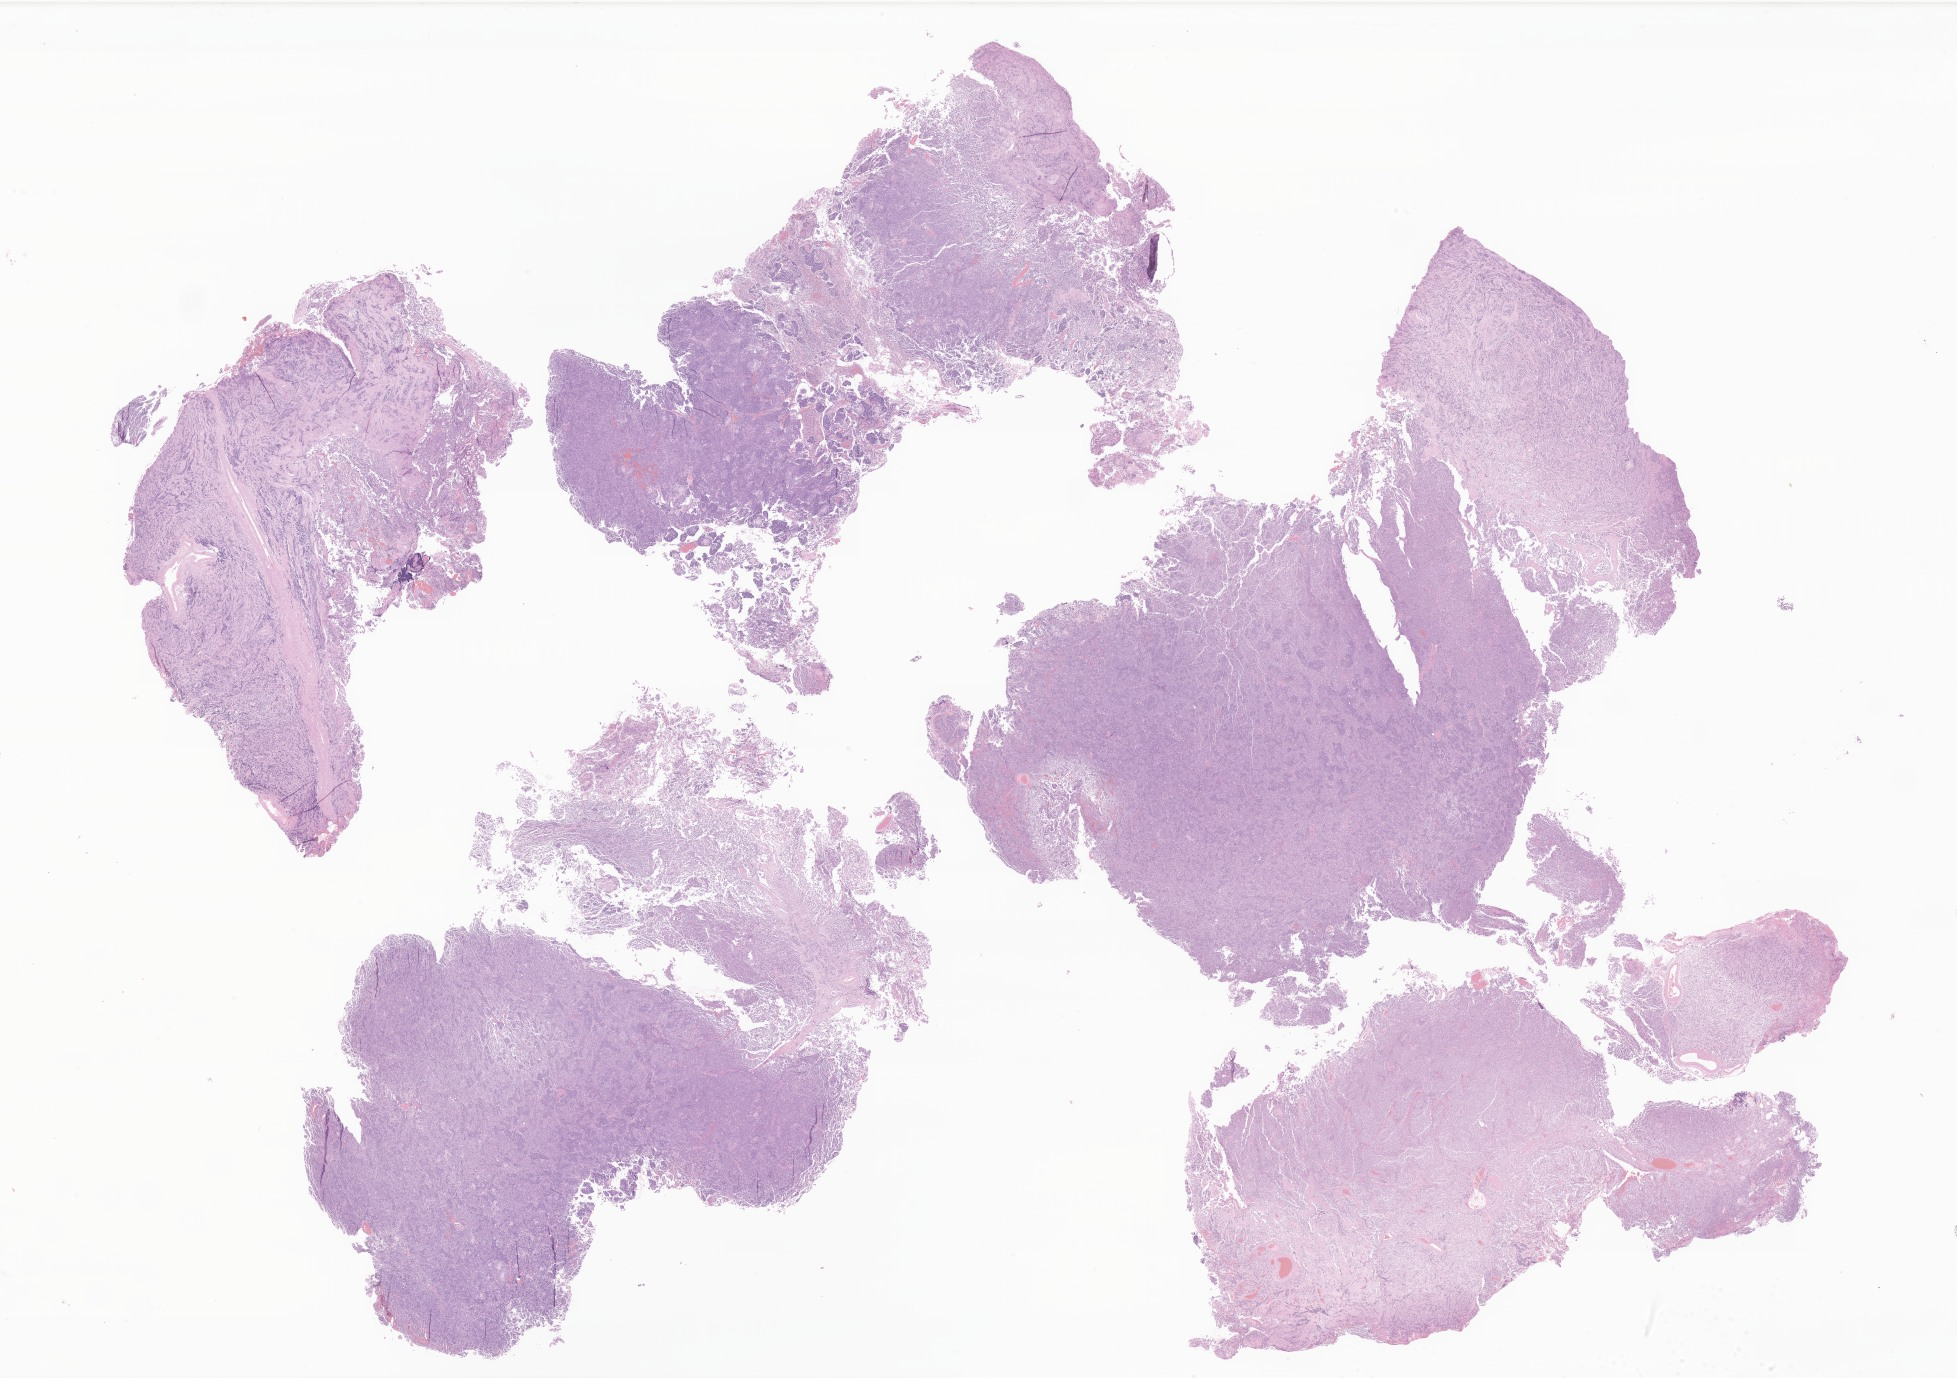
Whole-slide image, hematoxylin and eosin (H&E) stain of tumor tissue from the brain — whole scanned area (about 33.0 x 23.2 mm) shown as a low-resolution overview; formalin-fixed paraffin-embedded section. Patient: male, age 69 months (5 years 9 months).
Diagnosis (ICD-O-3 morphology term): Medulloblastoma, NOS.